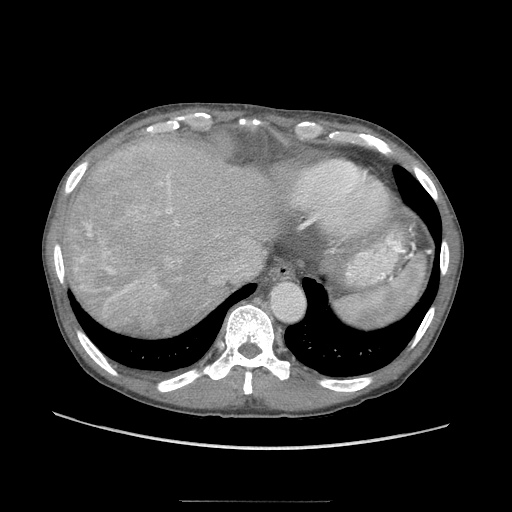
Contrast-enhanced abdominal CT (liver protocol), one axial slice; slice 81 of 103 in the series (ordered by position); reconstruction kernel STANDARD; soft-tissue window (W 400 / L 40 HU); 2.5 mm slice thickness; 512 × 512 image matrix, field of view 380 × 380 mm. From the clinical record (not read from this slice): diagnosis: hepatocellular carcinoma (patient treated with transarterial chemoembolisation; whether this scan precedes or follows treatment is not stated here); TNM stage (as recorded): Stage-IIIA; Child-Pugh class: A; tumour differentiation: moderately differentiated; tumour nodularity: multinodular.
Structures marked on this image (semi-automatic segmentation, software-assisted and operator-edited):
- abdominal aorta: bounding box <271,284,304,320> (left, top, right, bottom; pixels)
- liver parenchyma outside the tumour (the mass and vessels are separate outlines, so this box may not span the whole liver): <64,124,275,326>
- liver vessels: <91,128,156,286>